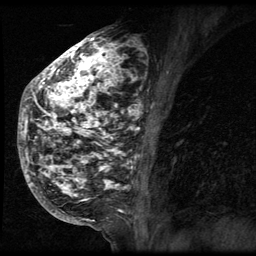
Breast MRI (dynamic contrast-enhanced), one sagittal slice. Position 31 of 64 along the scan axis. 3 images stored at this slice position (order not interpretable as contrast timing). 1.5 T. TE 4.2 ms, TR 9 ms. 2.5 mm slice thickness. 256 × 256 image matrix, field of view 180 × 180 mm. Patient: female, 50 years. From the clinical record (not read from this slice): setting: breast cancer imaged before/during neoadjuvant chemotherapy; receptor status: triple-negative.
Annotated regions visible in this slice (semi-automatic segmentation, software-assisted and operator-edited):
- analysis volume of interest (the breast-tissue region the enhancement analysis was run in; not a lesion): bounding box (x1, y1, x2, y2) in pixels: (24, 39, 140, 212)
- tumour enhancement mask (voxels above the 140 % enhancement threshold inside the analysis volume of interest): (24, 39, 140, 212)